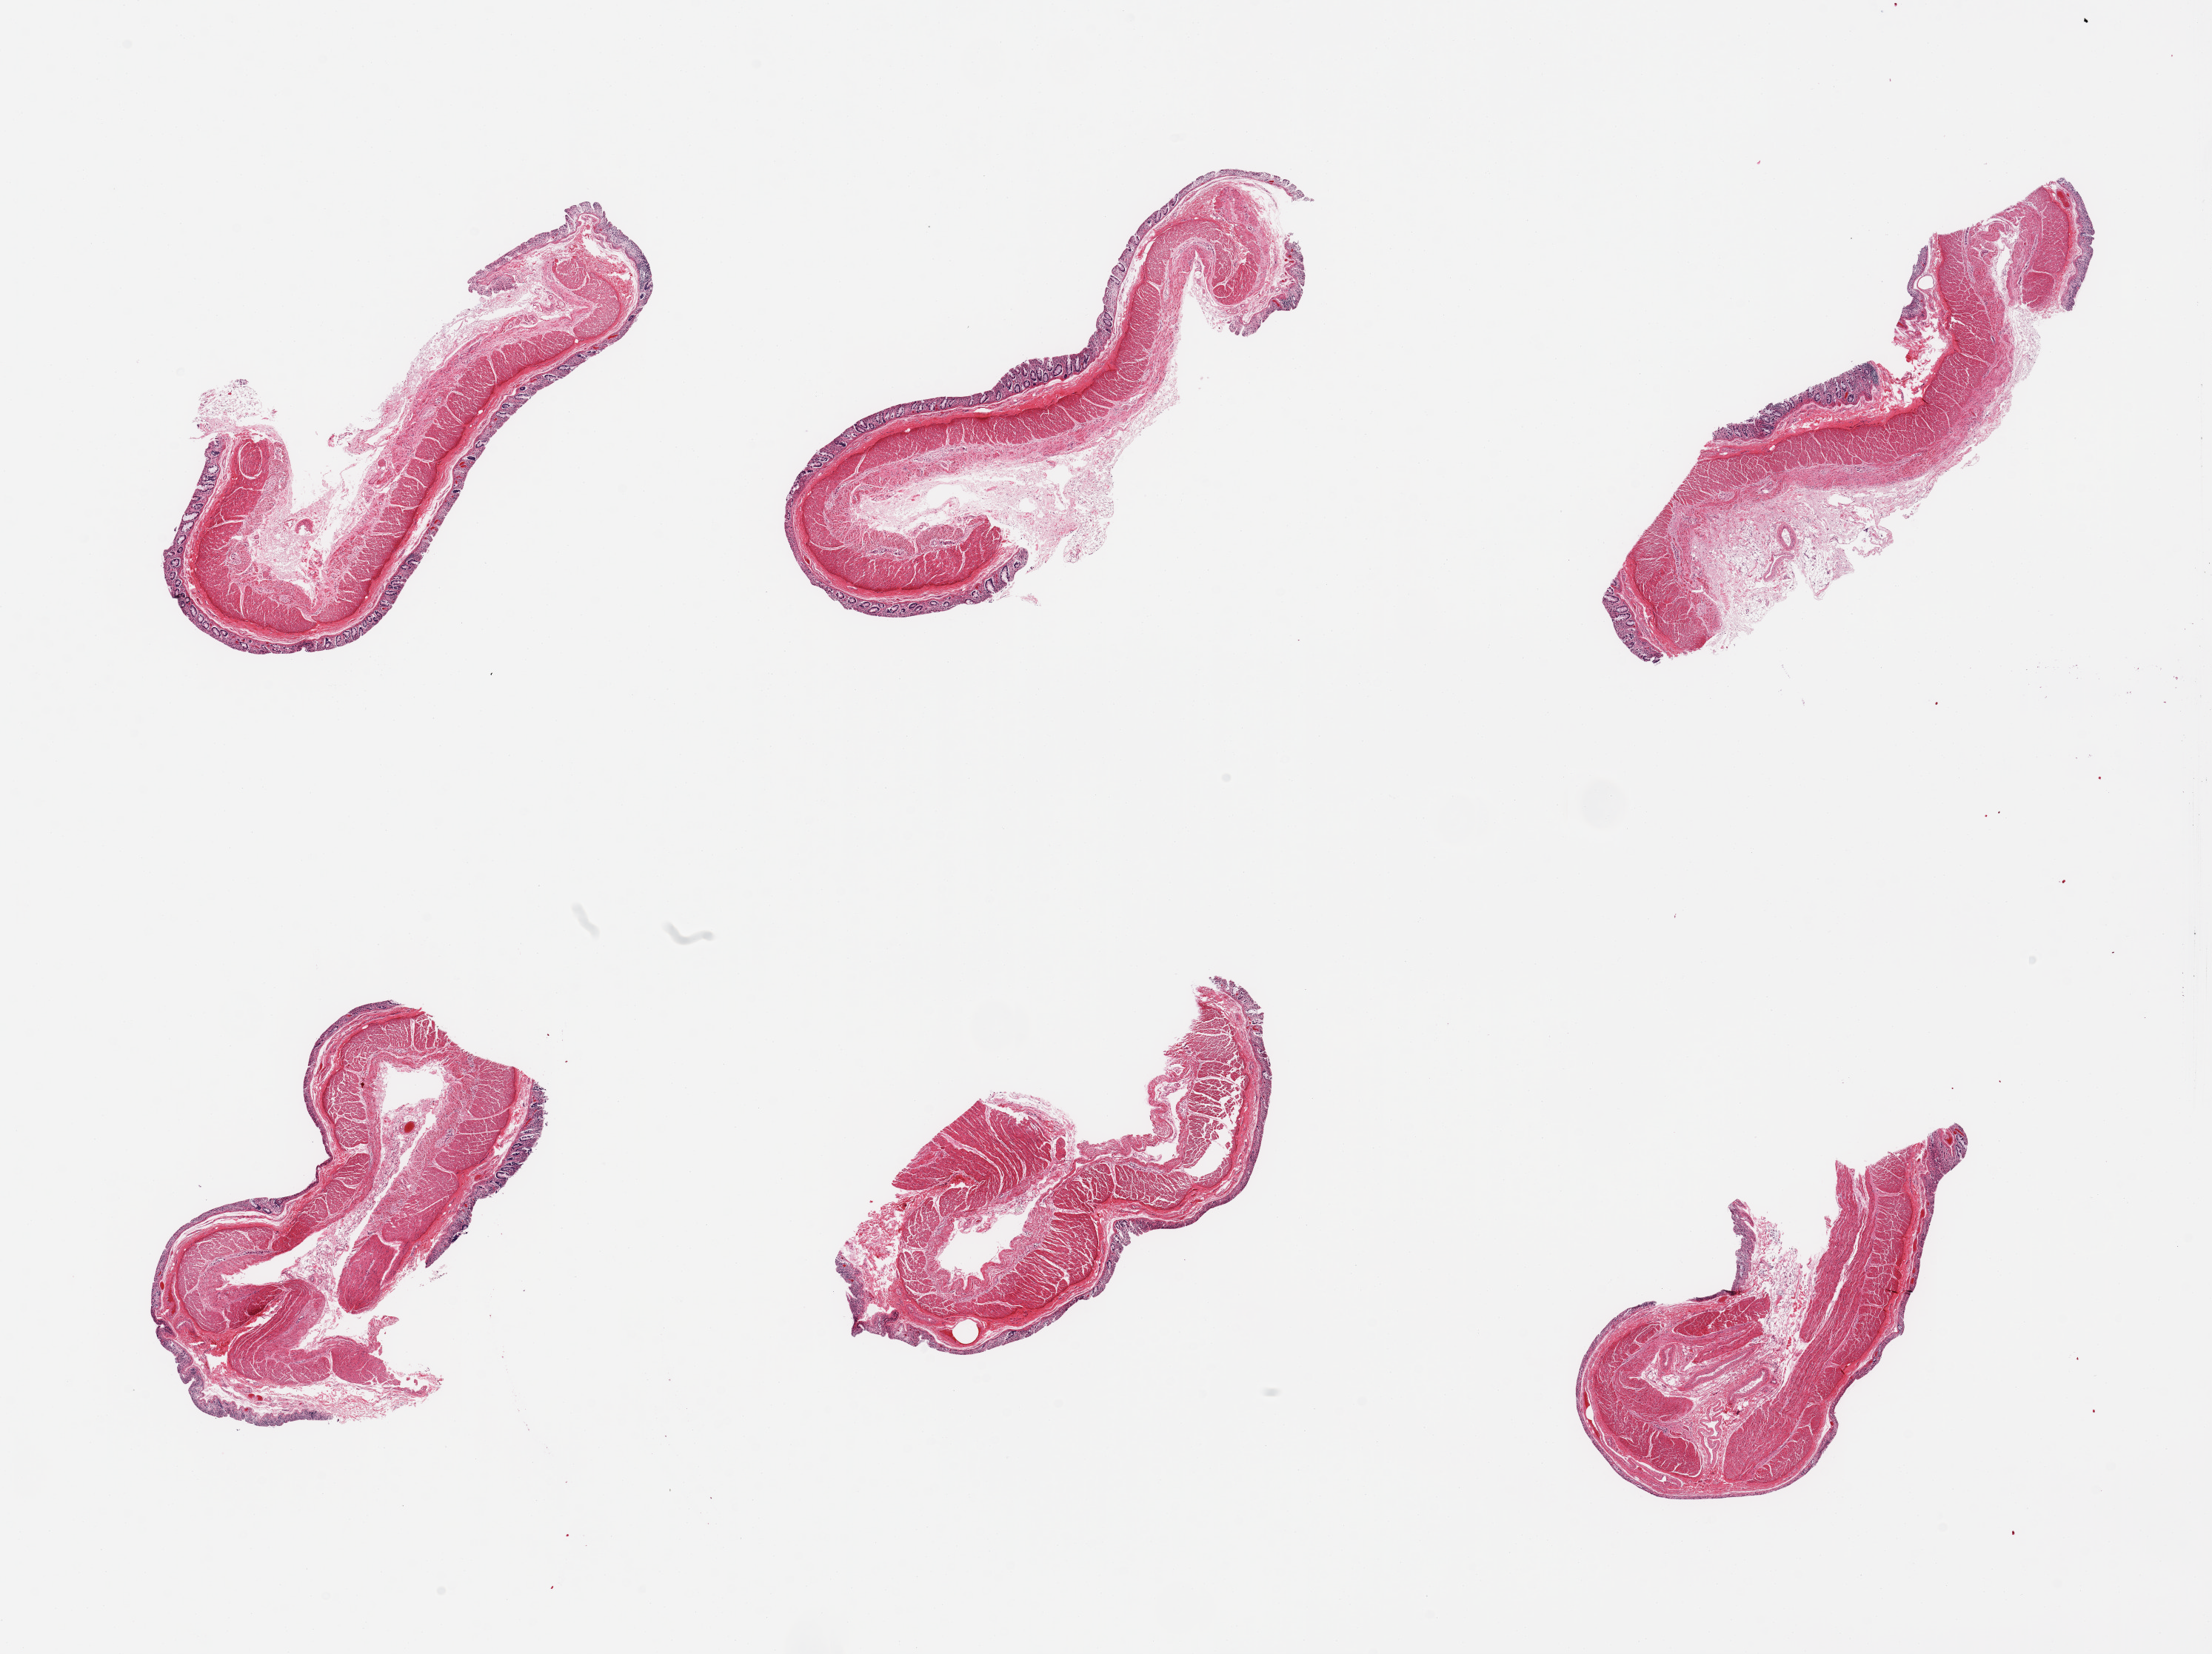
Digitized H&E-stained section, whole scanned area (about 23.6 x 17.7 mm) shown as a low-resolution overview; PAXgene-fixed, paraffin-embedded tissue; section of transverse colon (target tissue); tissue donor sample. Donor: male.
• reviewer comment on this tissue sample: 6 pieces; mucosa largely autolyzed, muscularis intact